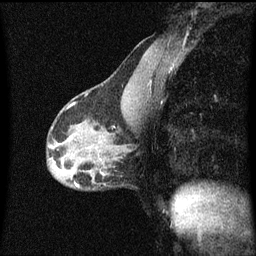
Breast MRI (dynamic contrast-enhanced), one sagittal slice; position 33 of 60 along the scan axis; dynamic contrast-enhanced series, image 2 of 3 at this slice position (ordered by acquisition); 1.5 T; TE 4.2 ms, TR 8.4 ms; 2 mm slice thickness; 256 × 256 image matrix, field of view 200 × 200 mm. Patient: female, 40 years.
Structures marked on this image (semi-automatic segmentation, software-assisted and operator-edited):
- analysis volume of interest (the breast-tissue region the enhancement analysis was run in; not a lesion): bounding box [x1, y1, x2, y2] px = [78, 166, 118, 191]
- tumour enhancement mask (voxels above the 70 % enhancement threshold inside the analysis volume of interest): [78, 172, 104, 187]